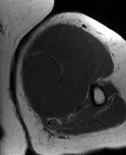
MRI of an extremity soft-tissue mass, one axial slice. MR volume resampled by the dataset authors to the PET/CT grid (not the native acquisition matrix). 3.27 mm slice thickness. 126 × 155 image matrix, field of view 123 × 151 mm. Female patient. From the clinical record (not read from this slice): histological type: pleiomorphic leiomyosarcoma; grade: high; site of the primary tumour: left biceps.
Structures marked on this image (expert contour drawn on MRI and transferred to this co-registered scan by the dataset authors):
- gross tumour volume including surrounding oedema: bounding box (x1, y1, x2, y2) in pixels: (20, 24, 105, 121)
- gross tumour volume (mass): (20, 24, 99, 119)